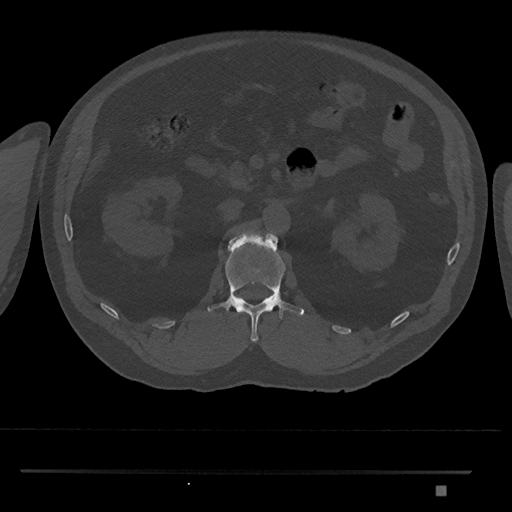
CT including the spine, one axial slice; slice 815 of 1134 in the series (ordered by position); reconstruction kernel Br40s/3; 120 kVp; bone window (W 1800 / L 400 HU); 0.5 mm slice thickness; 512 × 512 image matrix, field of view 429 × 429 mm. Patient: male, 65 years. From the clinical record (not read from this slice): primary cancer: prostate.
Structures marked on this image (semi-automatic segmentation, software-assisted and operator-edited):
- L1 vertebra: bounding box [x1, y1, x2, y2] px = [207, 230, 304, 343]